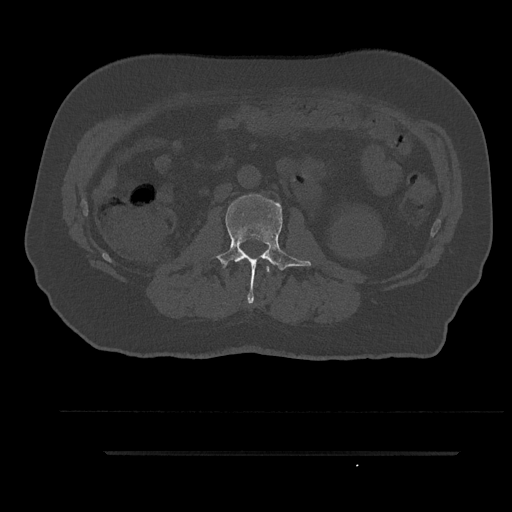
CT including the spine, one axial slice. Position 109 of 797 along the scan axis. Bone window (W 1800 / L 400 HU). 0.5 mm slice thickness. 512 × 512 image matrix. Patient: male, 63 years. Case-level facts recorded for this patient, not image findings: primary cancer: renal.
Outlined on this slice (semi-automatic segmentation, software-assisted and operator-edited):
- L1 vertebra: bounding box [x1, y1, x2, y2] px = [266, 266, 270, 273]
- L2 vertebra: [216, 194, 311, 303]